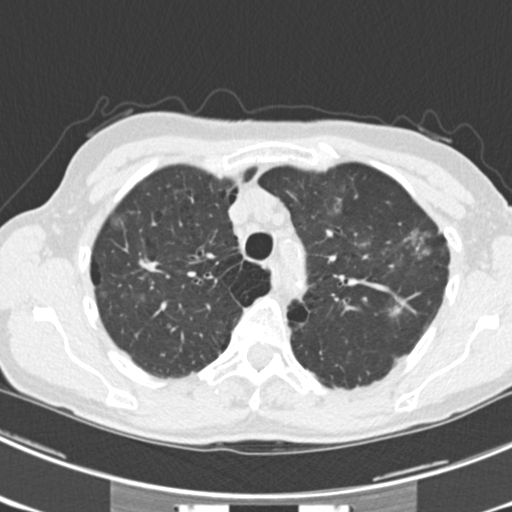
Low-dose screening chest CT, one axial slice. Position 172 of 225 along the scan axis. Lung window (W 1500 / L -600 HU). 512 × 512 image matrix.
Annotated regions visible in this slice (expert manual segmentation):
- lesion 3 (tumor, upper lobe of right lung): box from (x=146, y=261) to (x=157, y=266) px